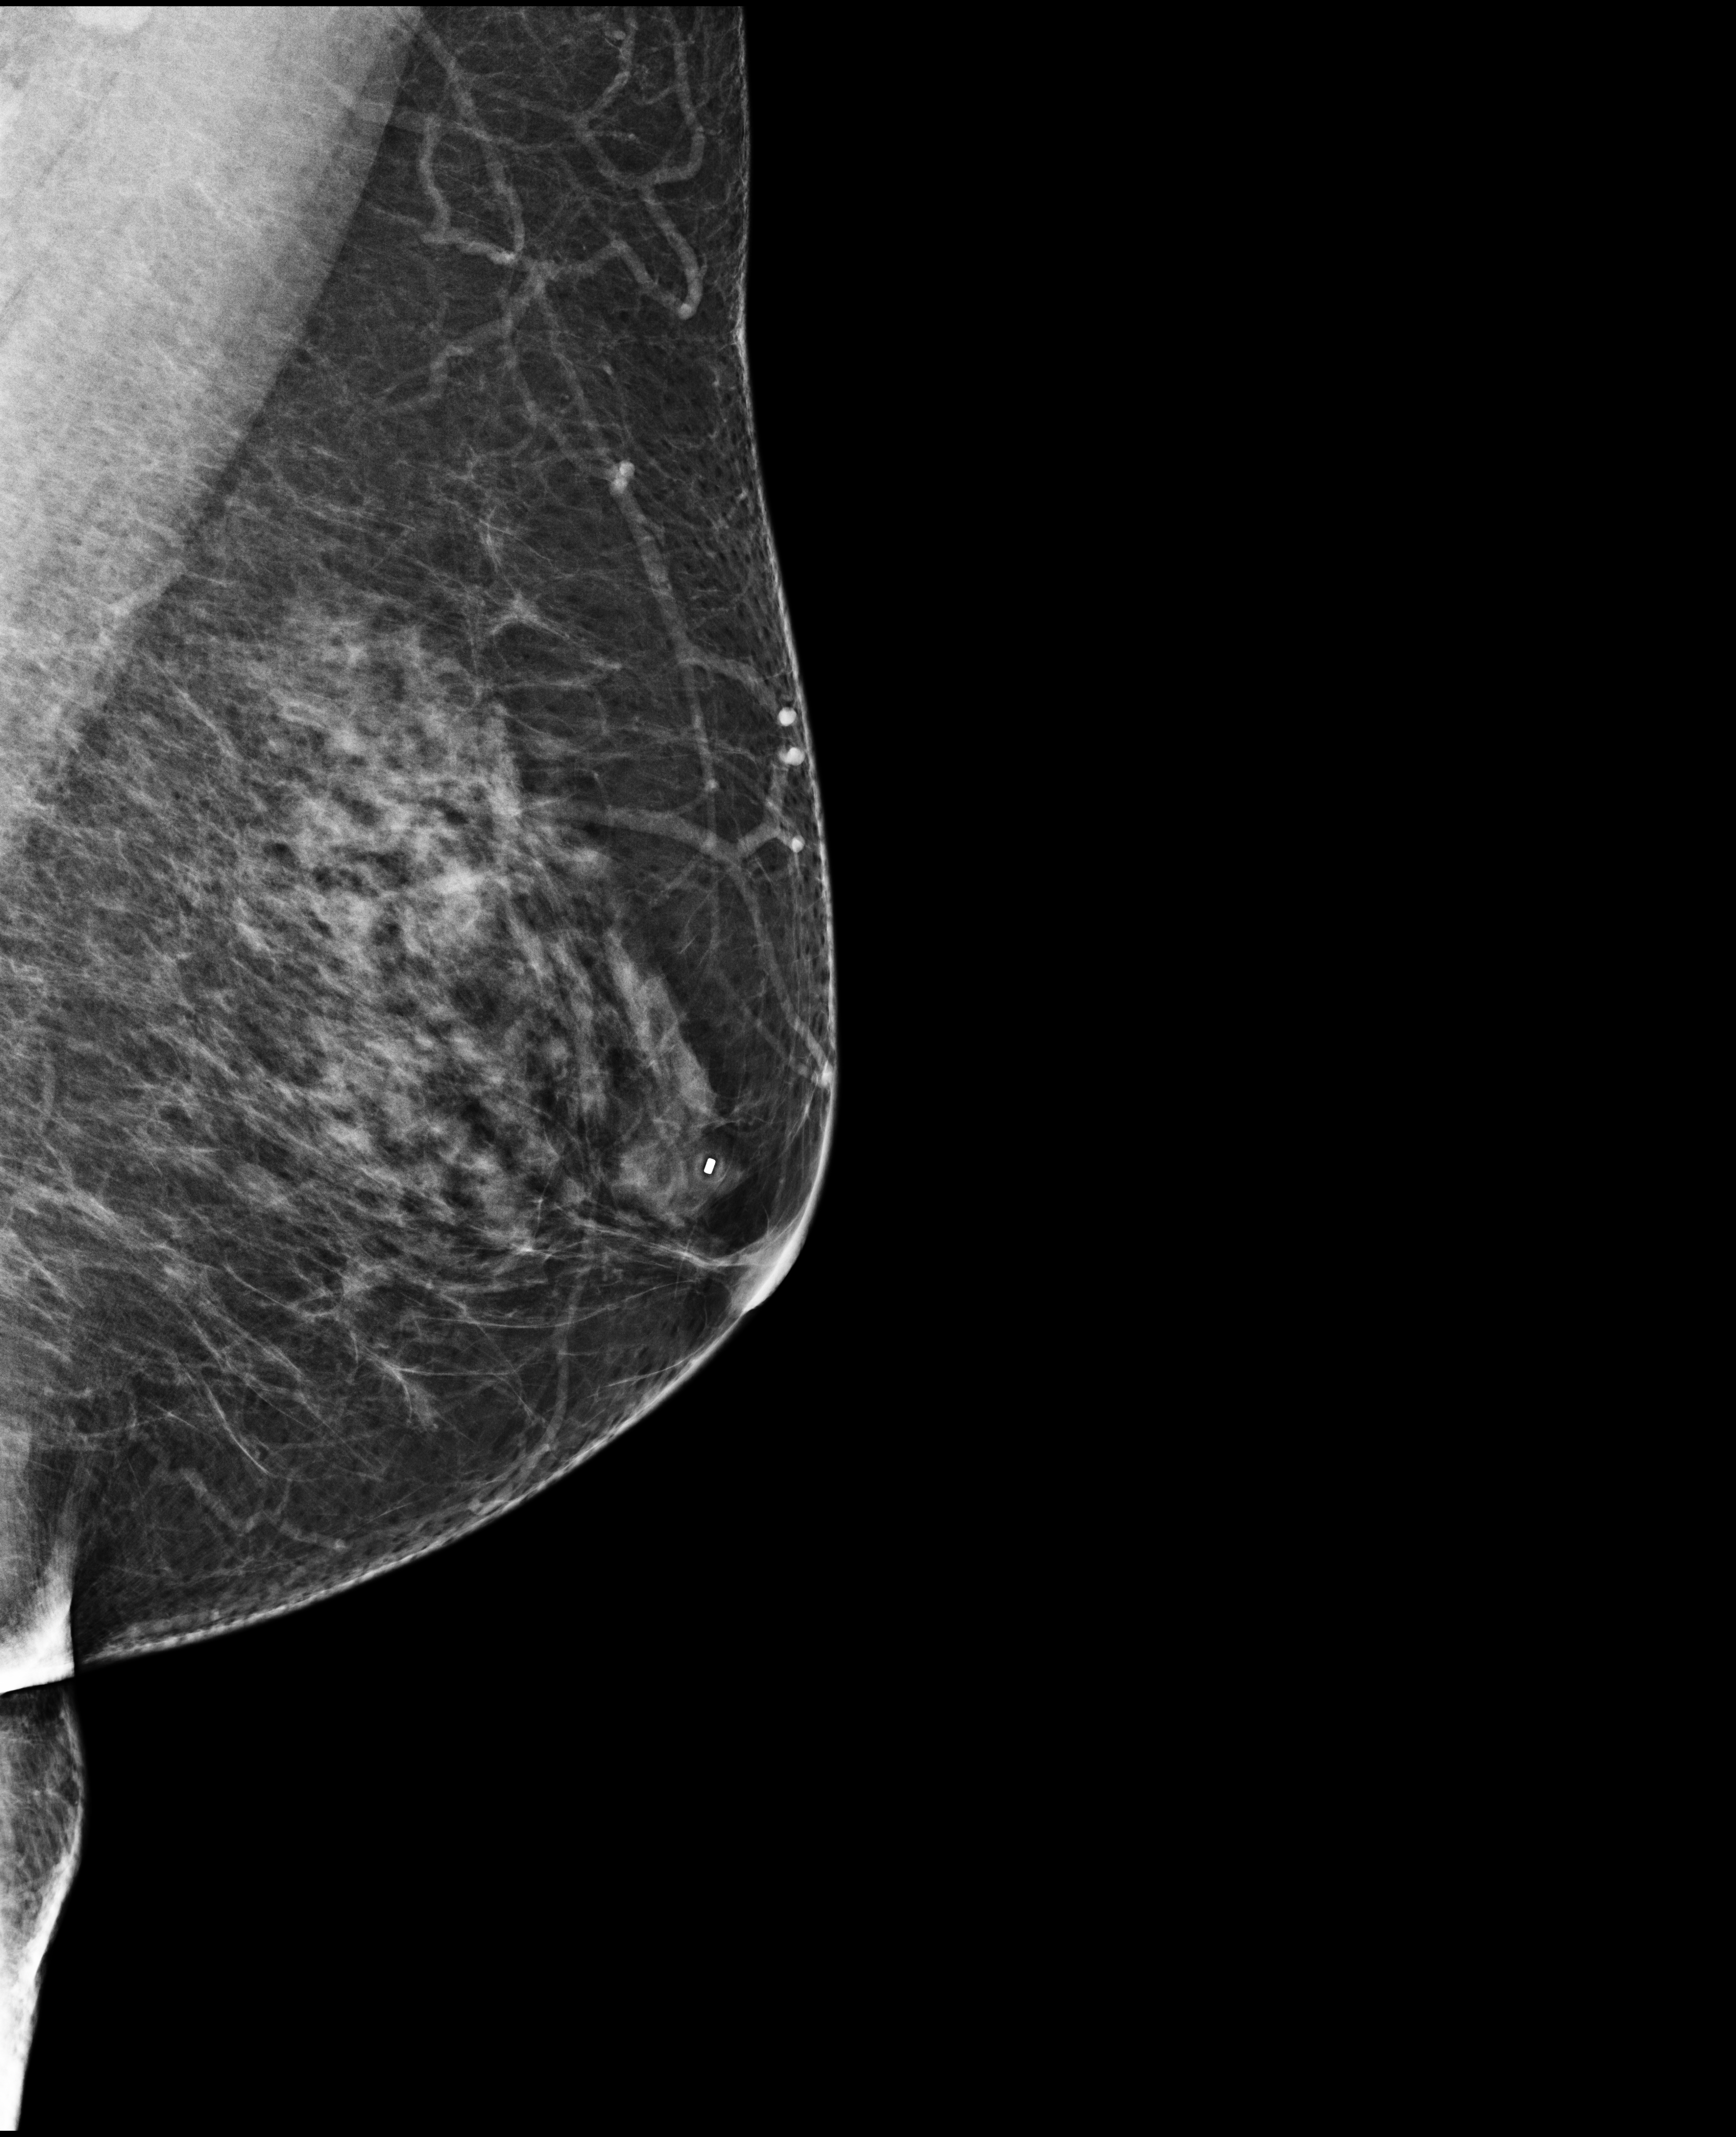
Annual screening mammography examination; system: Selenia Dimensions. Patient: female, 57 years.
Image type: full-field digital mammogram. Breast: left. Projection: MLO view.